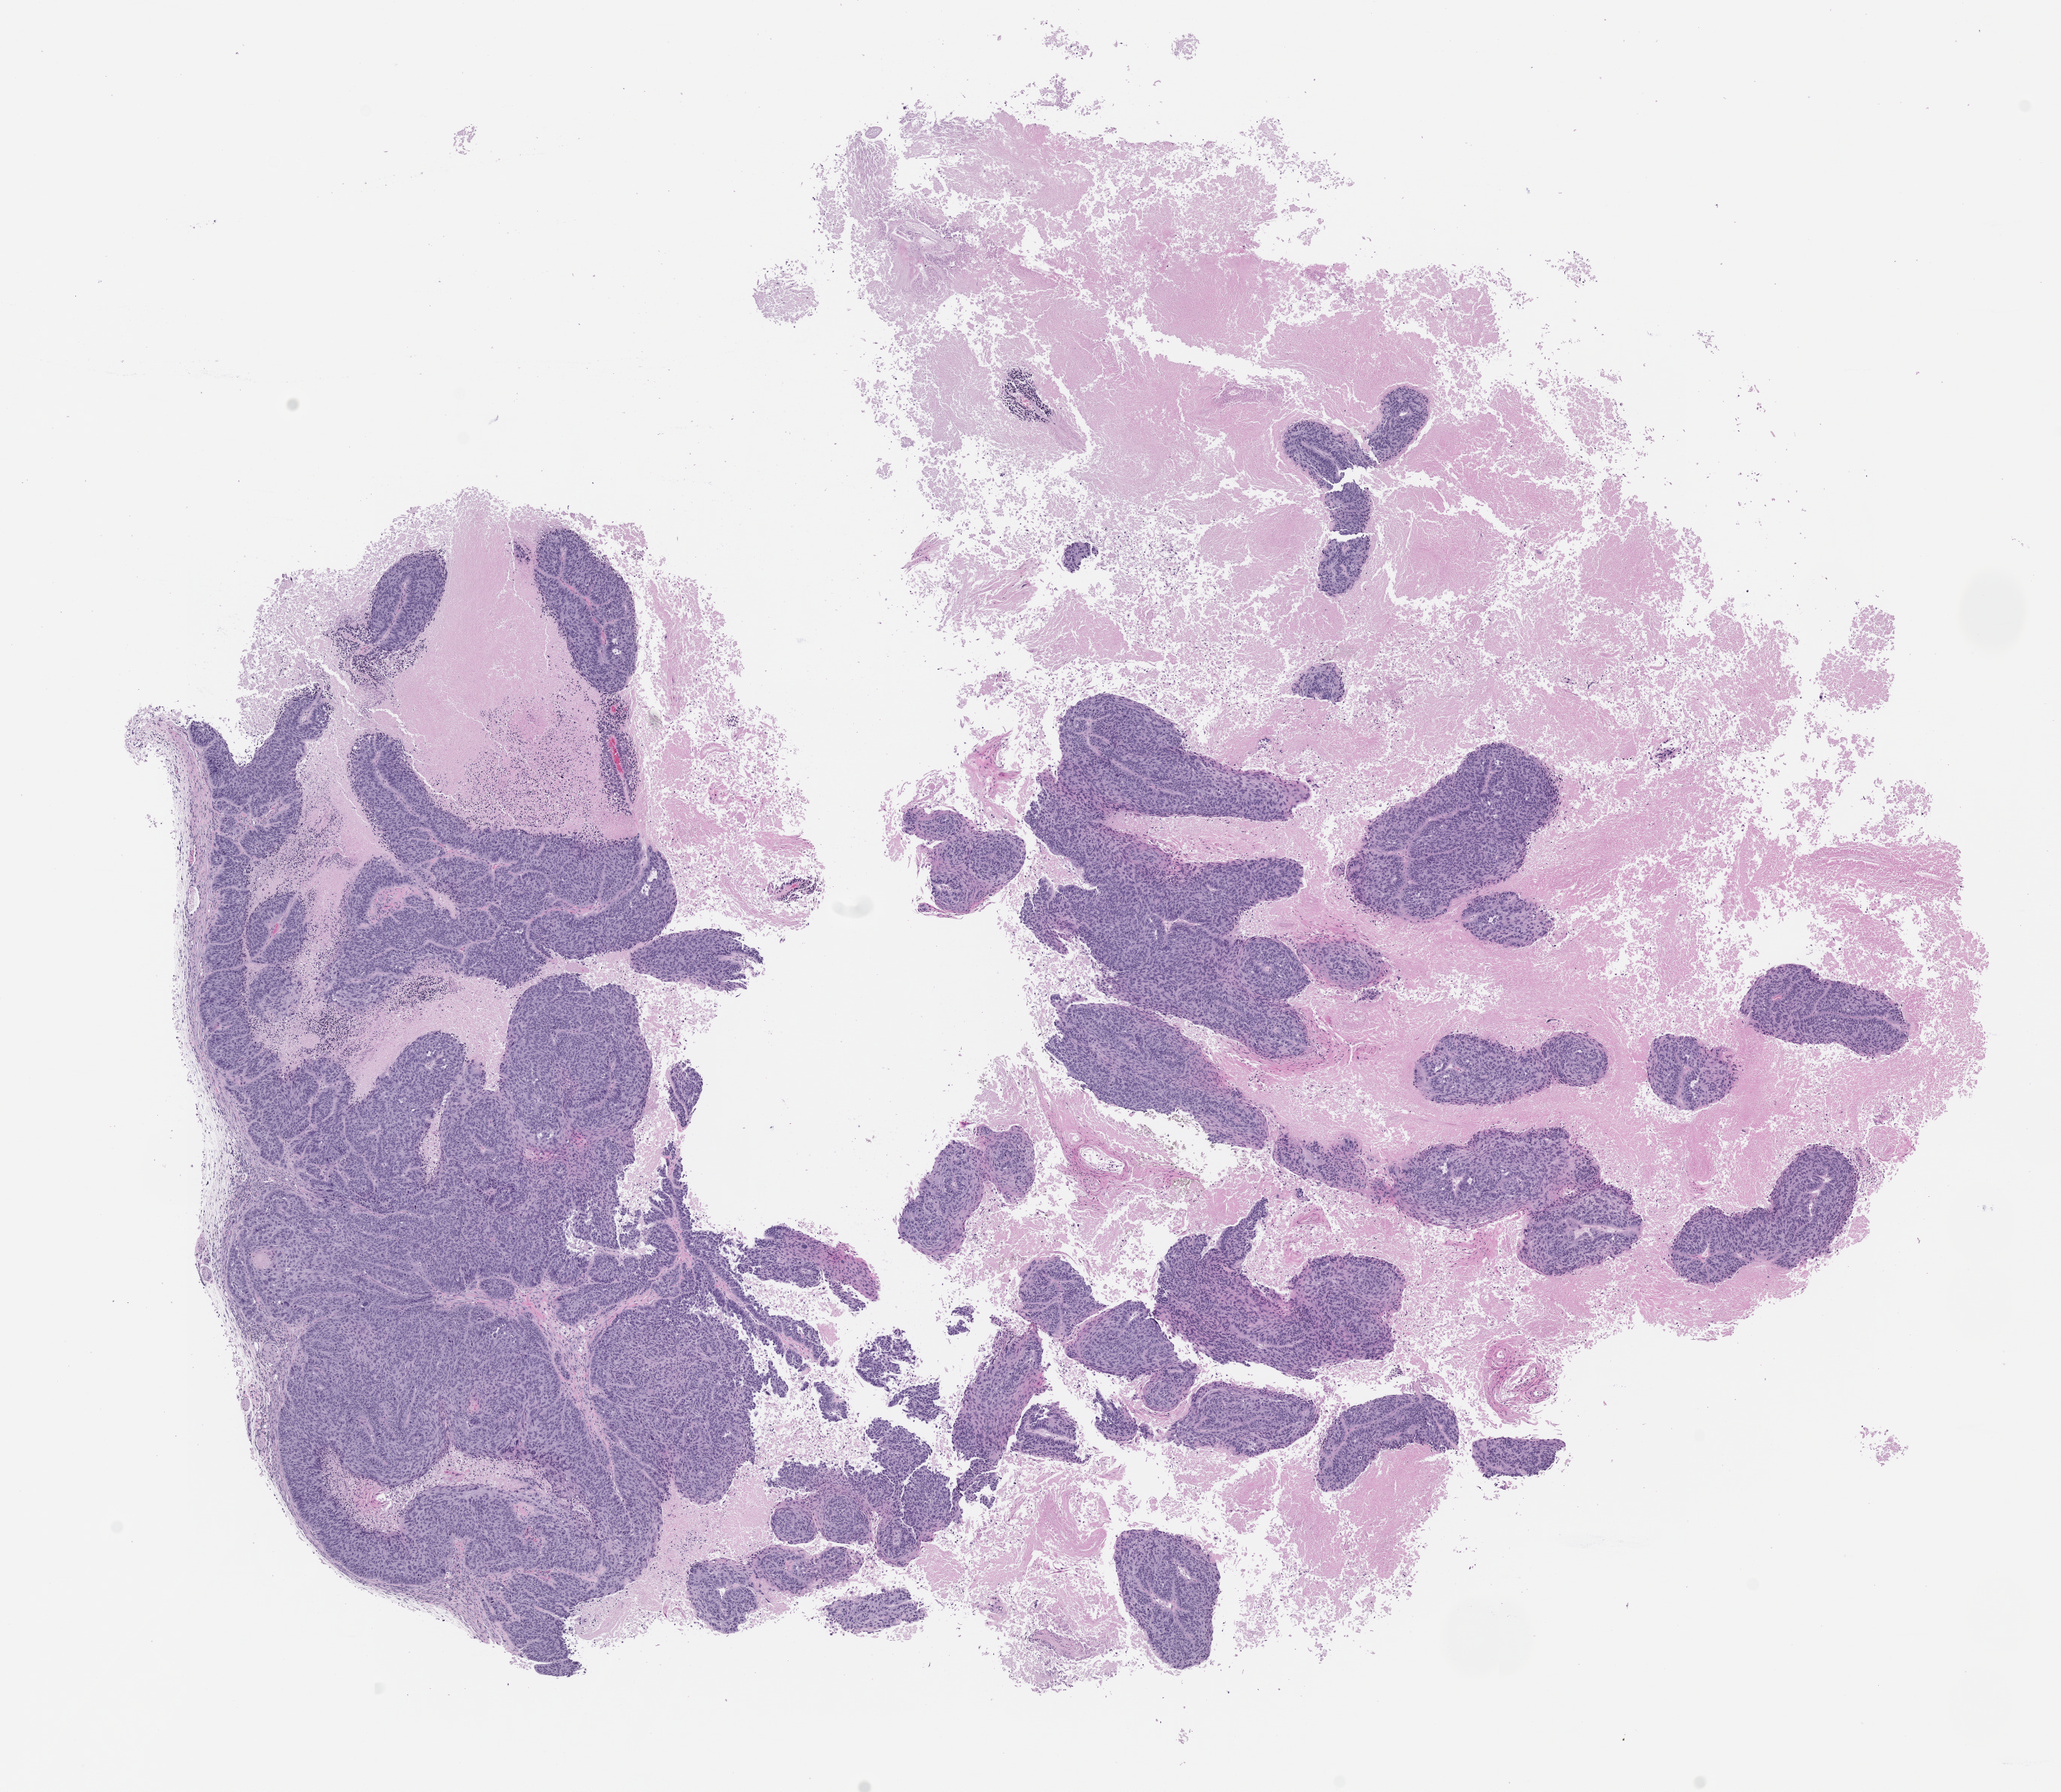
Whole-slide image, hematoxylin and eosin (H&E): patient-derived xenograft (human tumor grown in a mouse), low-resolution overview of the scanned area, about 11.0 x 9.6 mm; formalin-fixed paraffin-embedded section; tumor site category: lung.
Originating patient diagnosis: Lung Squamous Cell Carcinoma.